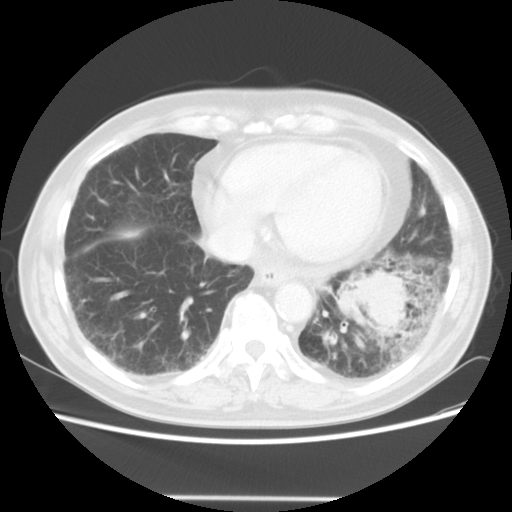
Chest CT, one axial slice. Position 14 of 56 along the scan axis. Reconstruction kernel STANDARD. 140 kVp. Lung window (W 1500 / L -600 HU). 5 mm slice thickness. 512 × 512 image matrix, field of view 360 × 360 mm. Patient: male, 66 years. From the clinical record (not read from this slice): clinical TNM (as recorded): T4 N3 M0; histopathological grade: G3.
Annotated regions visible in this slice (rectangle marked by the reading radiologist):
- lung tumour (recorded histology: small cell carcinoma): bounding box (x1, y1, x2, y2) in pixels: (334, 266, 407, 344)